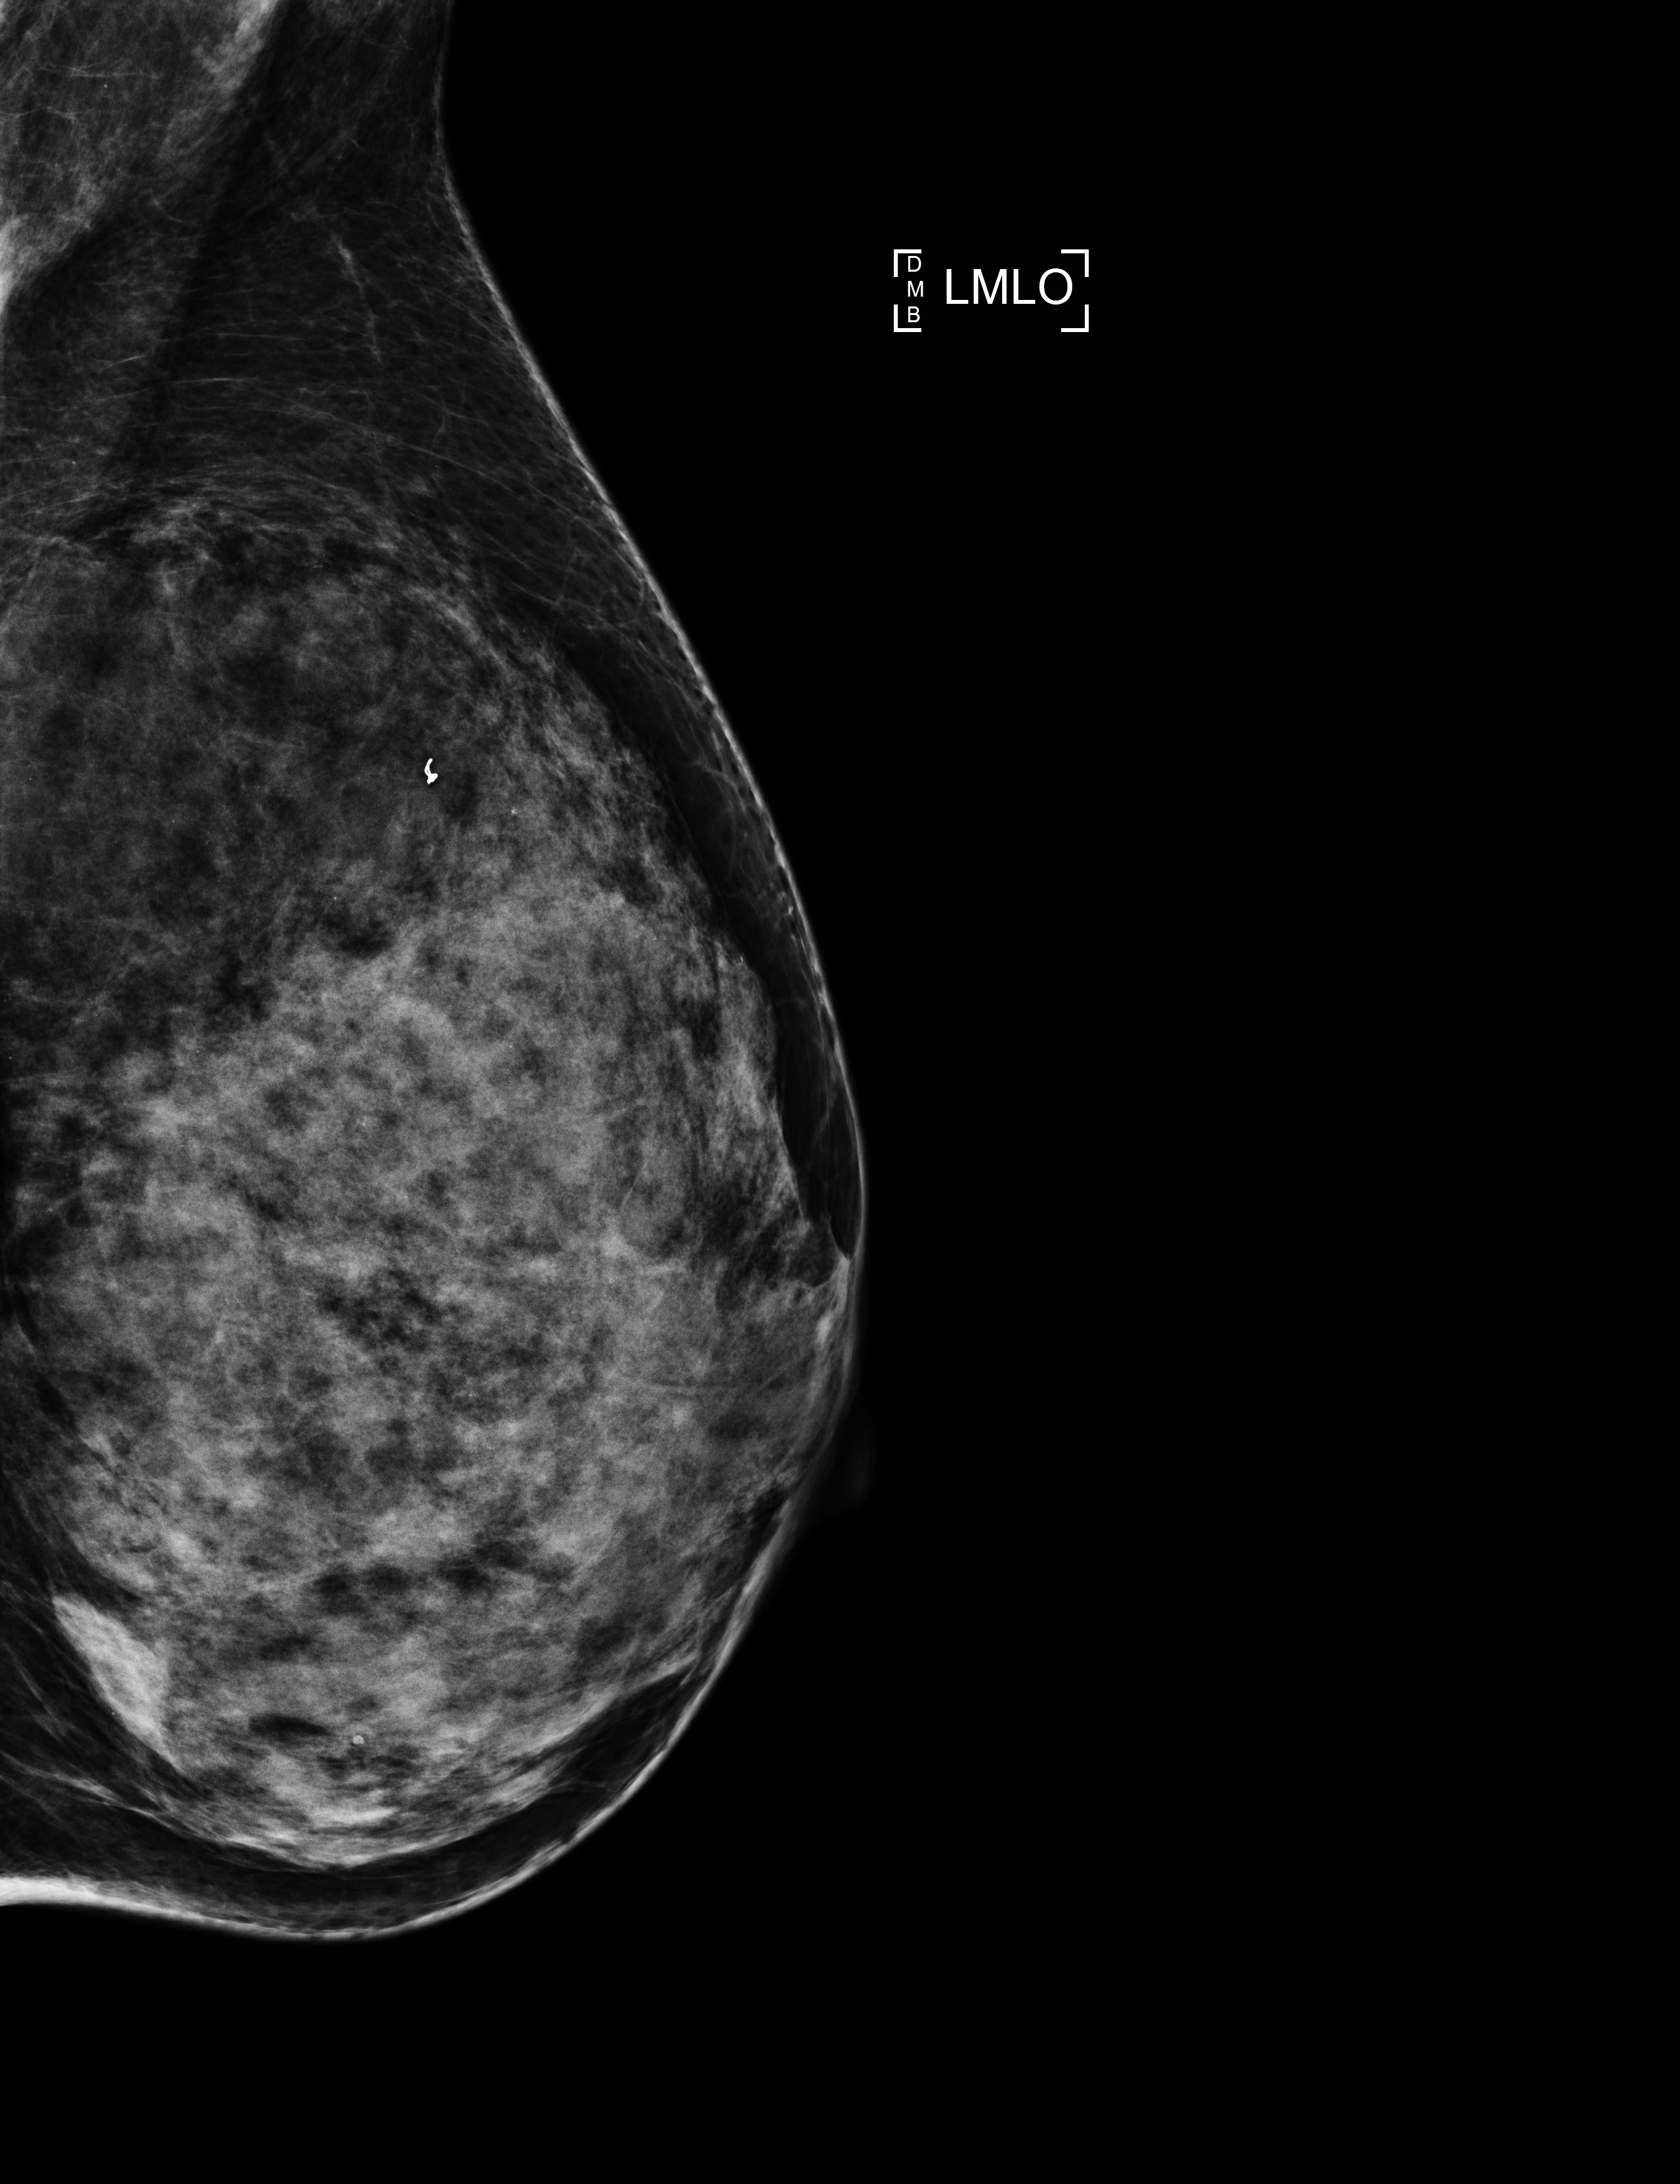
Screening examination. Female patient, age 62 years.
Image type: full-field digital mammogram. Breast: left. Projection: mediolateral oblique (MLO) view. BI-RADS breast density category at the screening exam (both breasts, scale 1–4): 4. Final BI-RADS category for the screening round (tomosynthesis exam, both breasts): category 1. Recall: no recall after this screen.